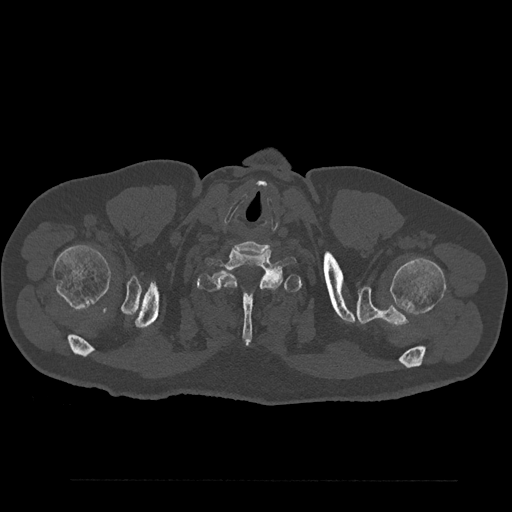
CT including the spine, one axial slice. Position 769 of 797 along the scan axis. Reconstruction kernel Br40s/3. 120 kVp. Bone window (W 1800 / L 400 HU). 512 × 512 image matrix, field of view 430 × 430 mm. Patient: male, 61 years. Case-level facts recorded for this patient, not image findings: primary cancer: prostate.
Annotated regions visible in this slice (semi-automatically segmented with operator editing):
- T1 vertebra: bounding box <197,259,302,345> (left, top, right, bottom; pixels)